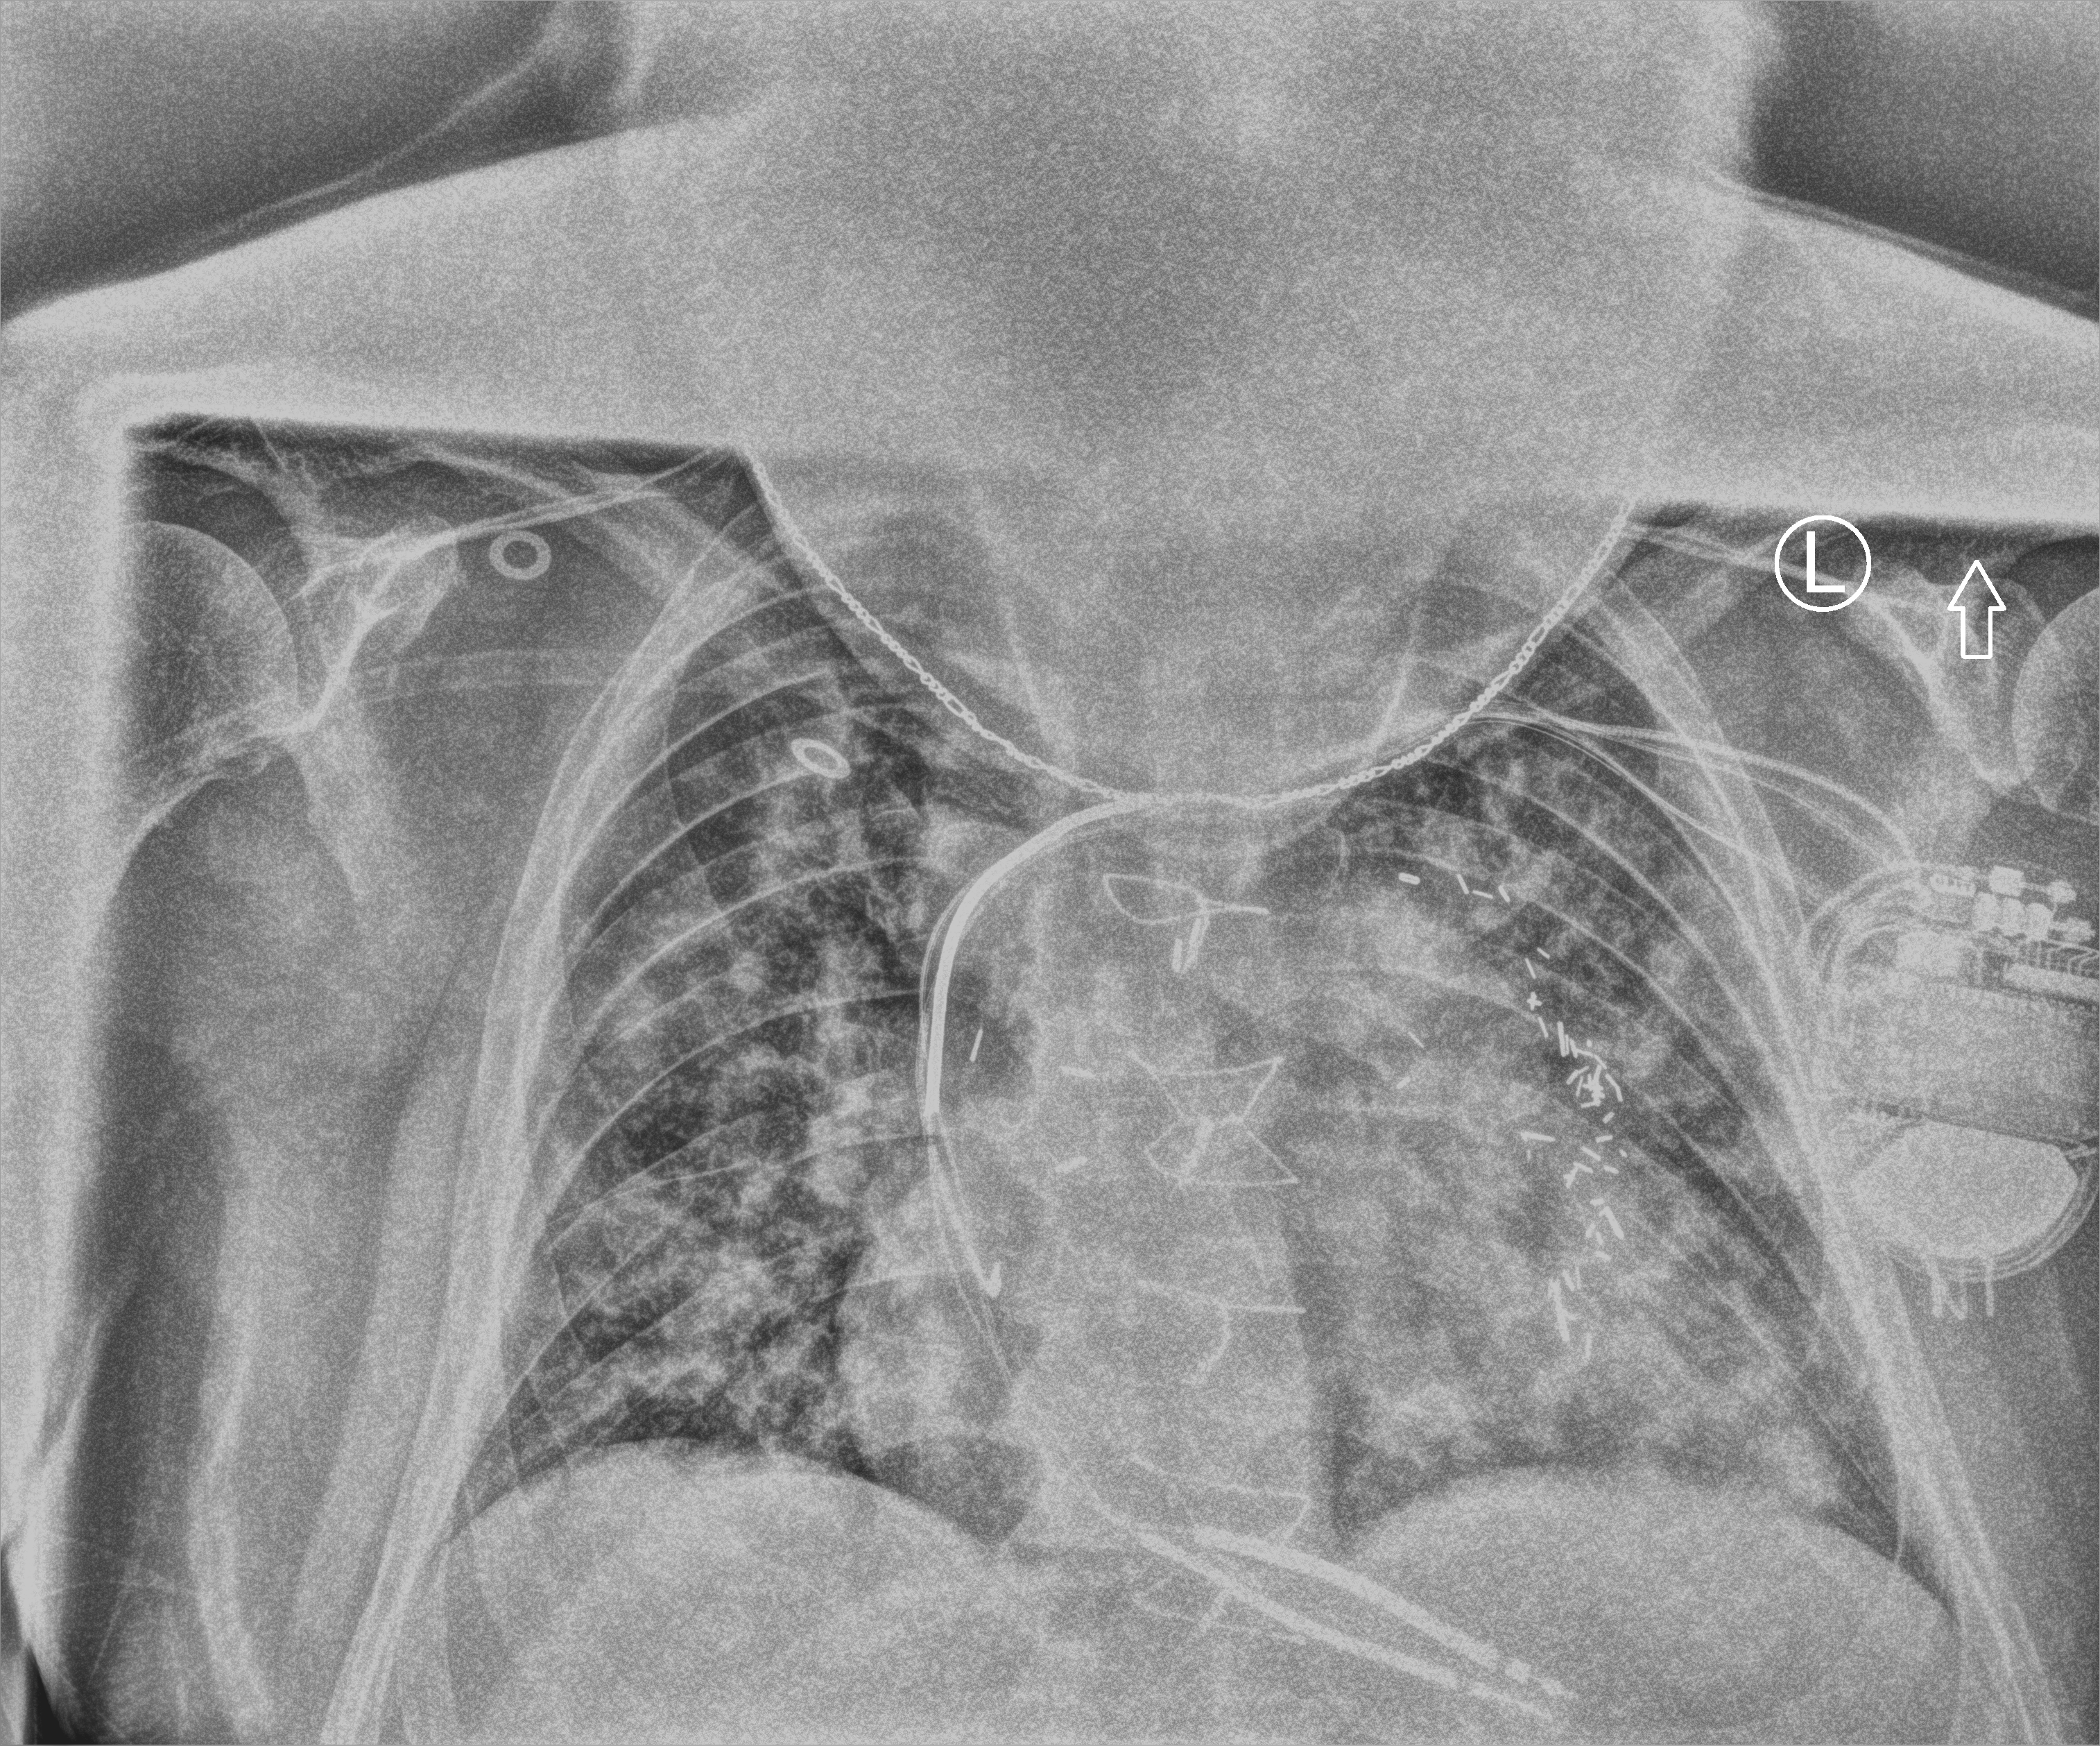
Chest X-ray (portable), anteroposterior (AP) projection. Male patient hospitalised with COVID-19, age 60–74 years.
Hospital-stay facts (about this admission, not read from this image; timing relative to this image not recorded): admitted to intensive care during this hospital stay: yes.